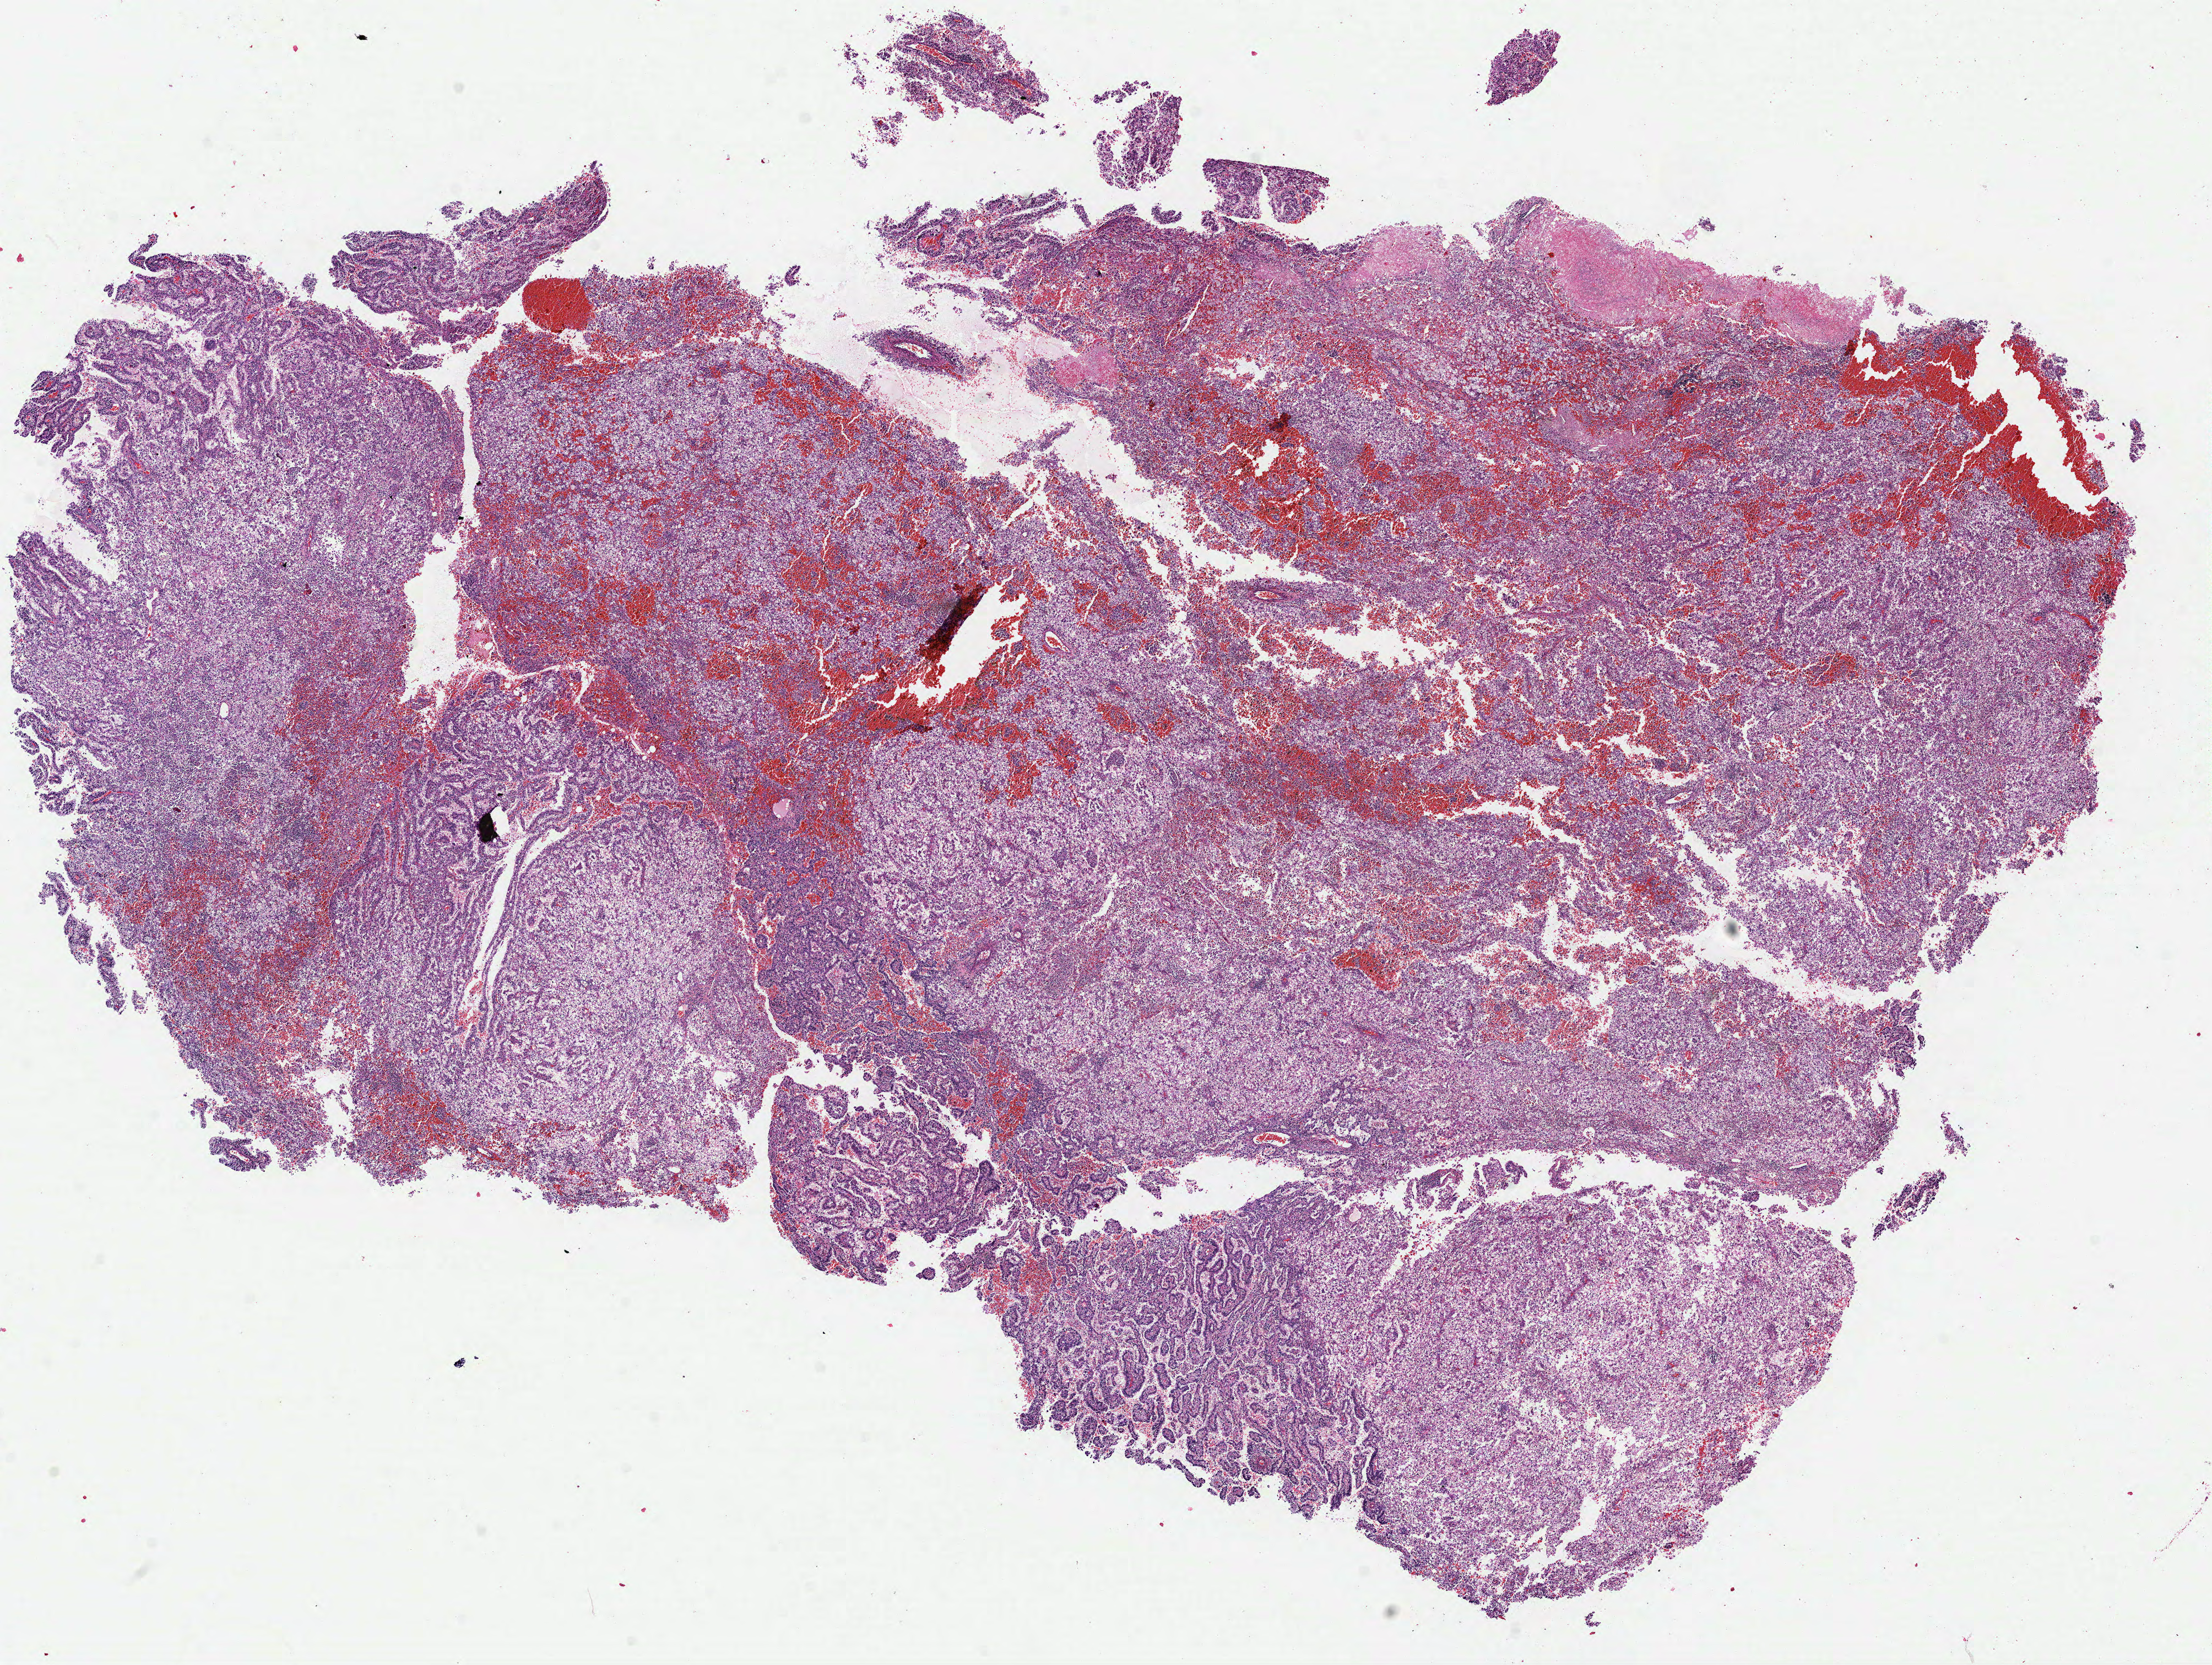
Hematoxylin and eosin (H&E) stained whole-slide image — low-resolution overview of the scanned area, about 16.2 x 12.2 mm (acquisition: 40x scan). Formalin-fixed paraffin-embedded (FFPE) diagnostic section. Primary tumour sample from the kidney. Patient: female, age at initial diagnosis 64 years. Histologic grade: G2 (moderately differentiated).
• TNM: T1 N0 M0
• histologic diagnosis: Clear cell adenocarcinoma, NOS
• lymph nodes positive (case pathology): 0 of 7 examined
• AJCC pathologic stage: I